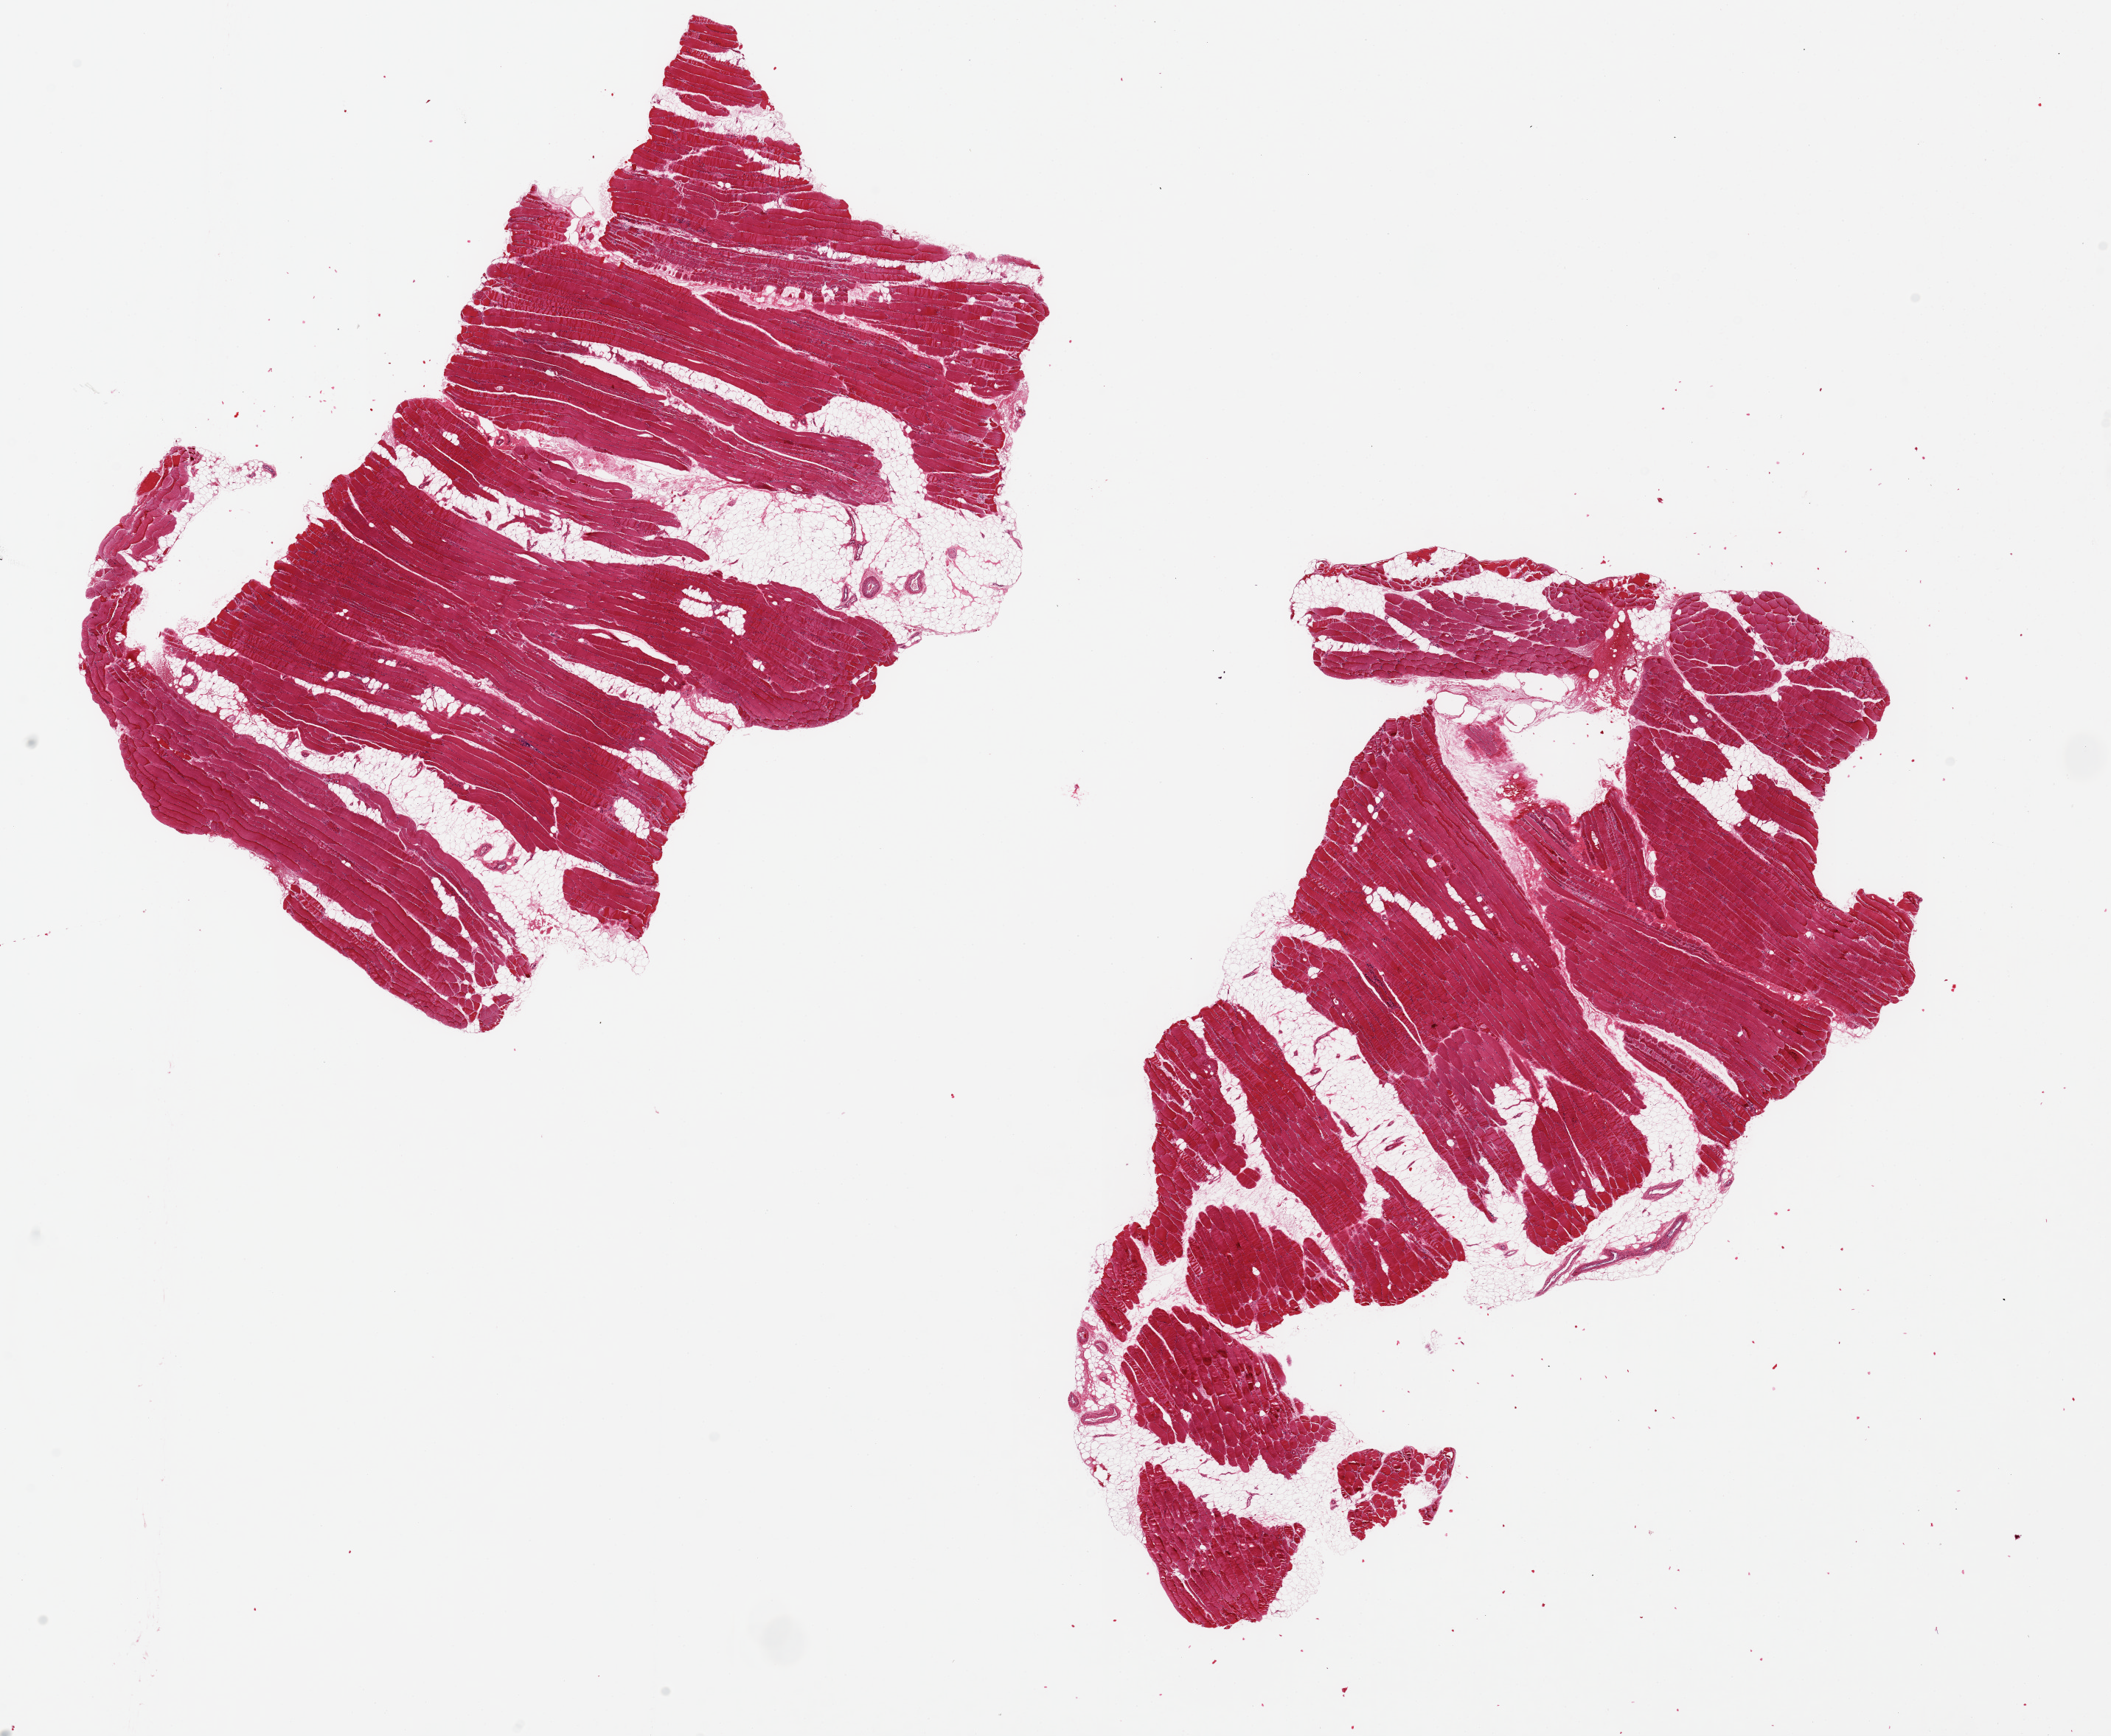
Whole-slide image, haematoxylin and eosin stain — low-resolution overview of the scanned area, about 22.6 x 18.6 mm (from a 20x scan); PAXgene-fixed paraffin-embedded (PFPE) section; section of skeletal muscle (target tissue); tissue donor sample. Donor: female.
Pathologist's review note for this sample: 2 pieces 11x8 & 13x8mm; Fatty infiltration among muscle fibers and degenerating fibers probably due to chronic ischemia and atrophy.